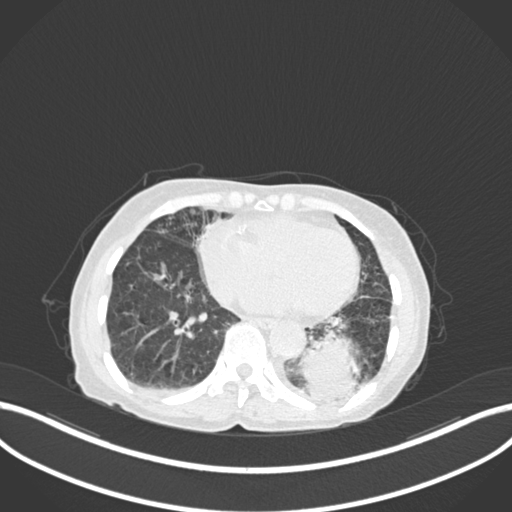
Chest CT, one axial slice. Position 40 of 233 along the scan axis. Reconstruction kernel B30f. Lung window (W 1500 / L -600 HU). 1 mm slice thickness. 512 × 512 image matrix, field of view 400 × 400 mm. Female patient, age 78 years. From the clinical record (not read from this slice): clinical TNM (as recorded): T3 N0 M1.
Structures marked on this image (bounding box drawn by a radiologist):
- lung tumour (recorded histology: squamous cell carcinoma): bounding box <298,328,363,394> (left, top, right, bottom; pixels)